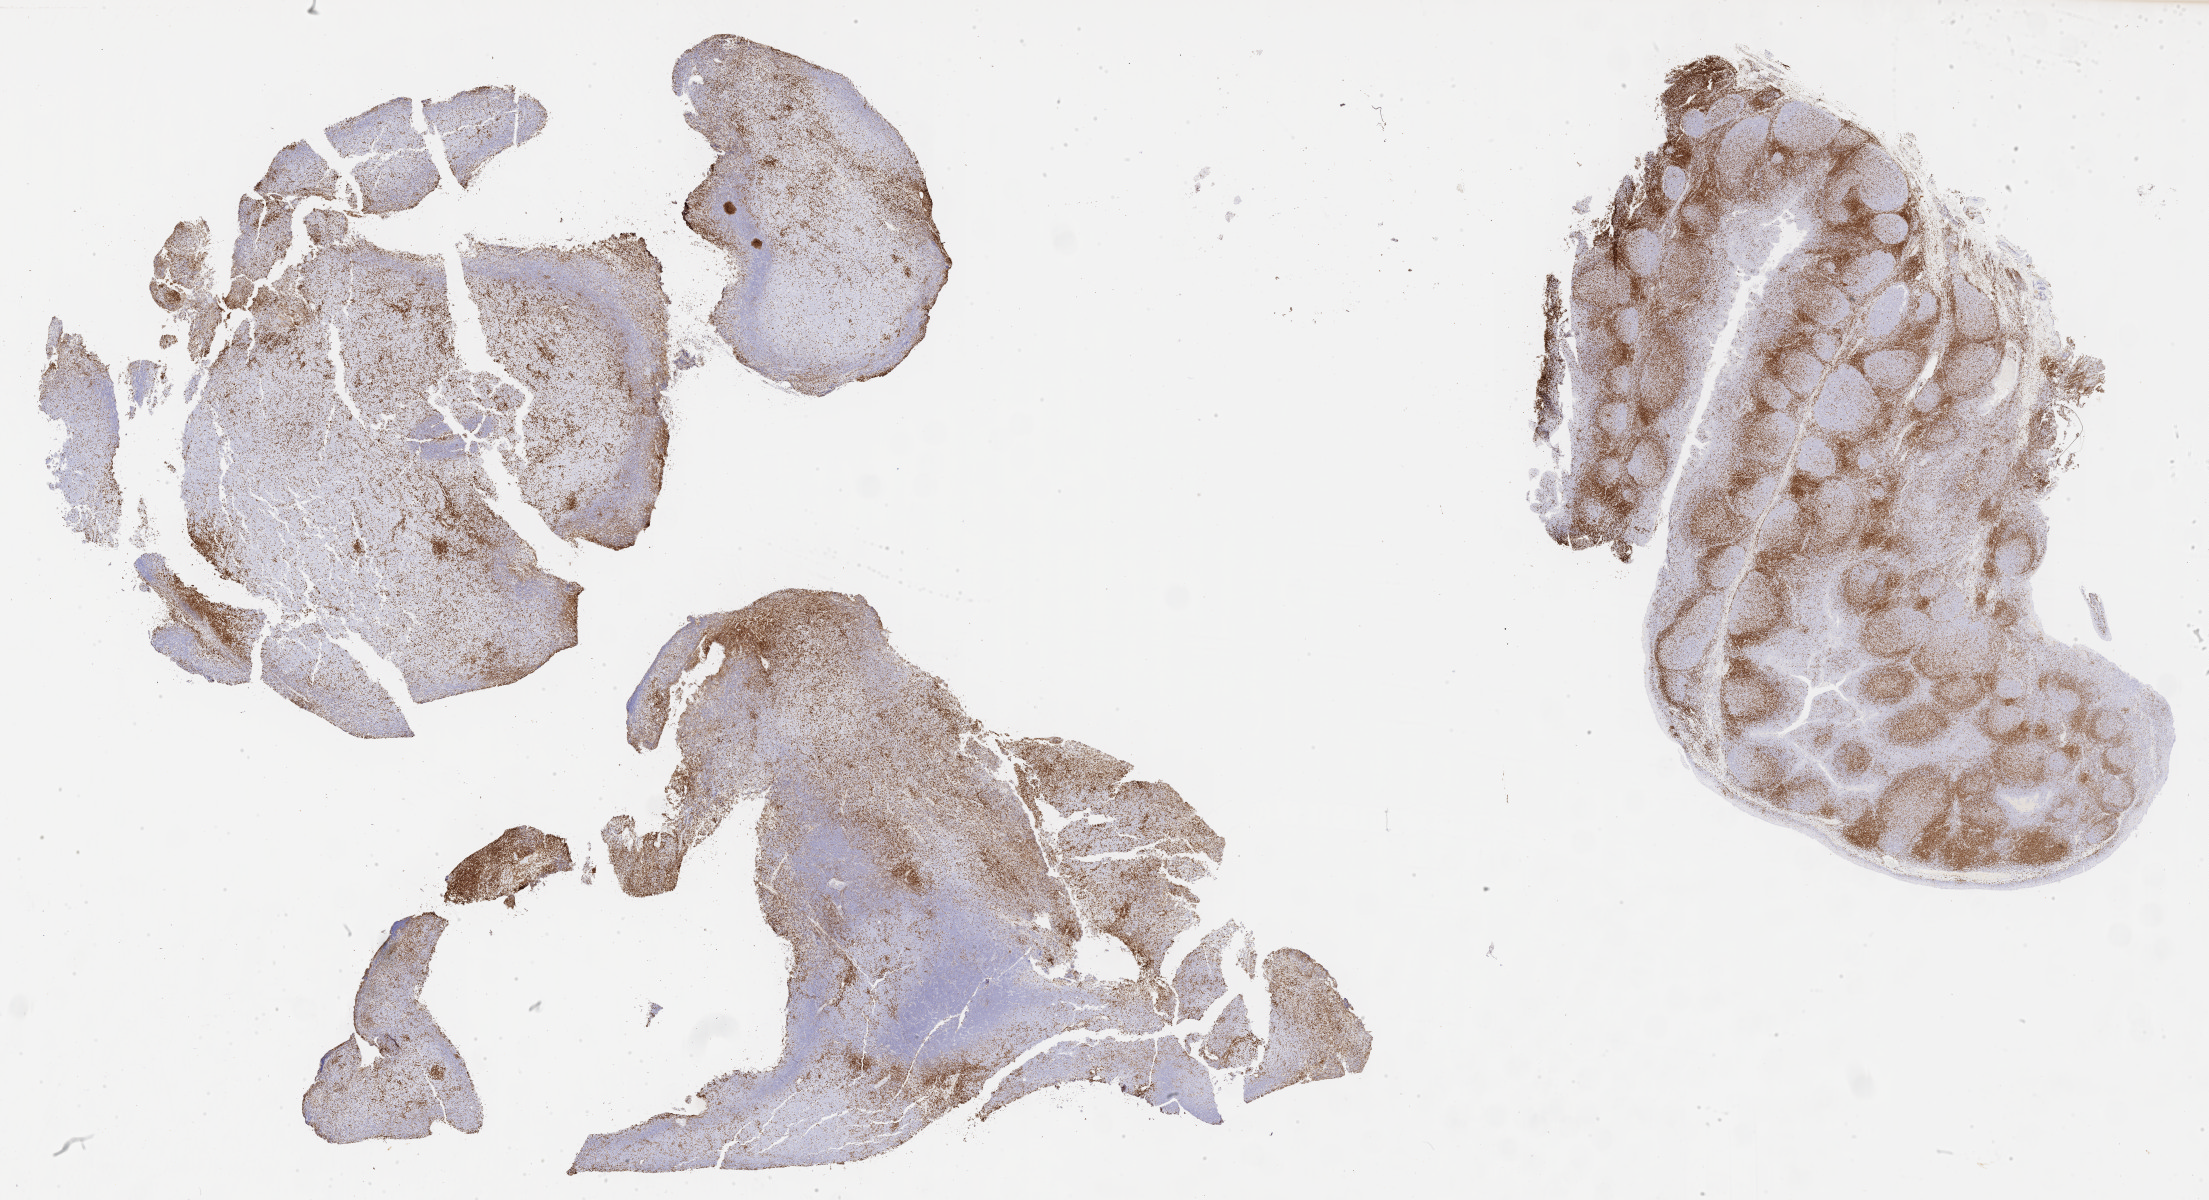
Whole-slide image, immunohistochemical stain for CD3, whole scanned area (about 35.7 x 19.4 mm) shown as a low-resolution overview; specimen: tumor tissue; anatomic site: liver. Patient male; 45 years old.
Histologic diagnosis: Diffuse large B-cell lymphoma, NOS.